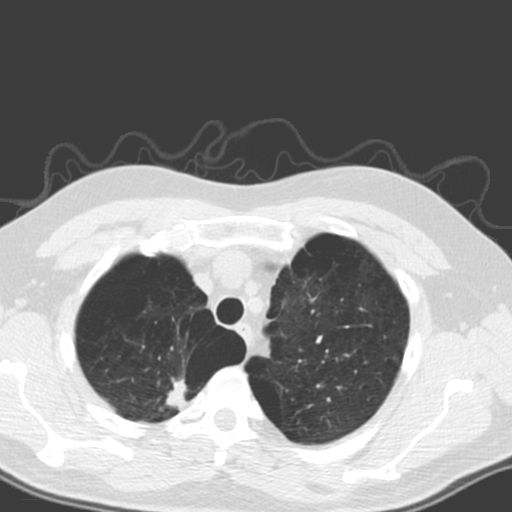
Low-dose screening chest CT, one axial slice; position 142 of 173 along the scan axis; lung window (W 1500 / L -600 HU); 3.2 mm slice thickness; 512 × 512 image matrix, field of view 340 × 340 mm.
Structures marked on this image (expert manual segmentation):
- lesion 1 (tumor, upper lobe of right lung): bounding box (x1, y1, x2, y2) in pixels: (166, 378, 187, 411)